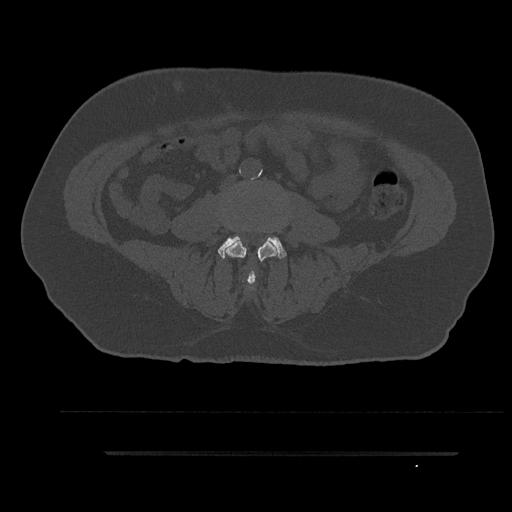
CT including the spine, one axial slice. Reconstruction kernel Br40s/3. 120 kVp. Bone window (W 1800 / L 400 HU). 0.5 mm slice thickness. 512 × 512 image matrix, field of view 432 × 432 mm. Male patient, age 63 years. From the clinical record (not read from this slice): primary cancer: renal.
Annotated regions visible in this slice (semi-automatic segmentation, software-assisted and operator-edited):
- L3 vertebra: box from (x=225, y=238) to (x=277, y=285) px
- L4 vertebra: (x=218, y=236)–(x=287, y=259)